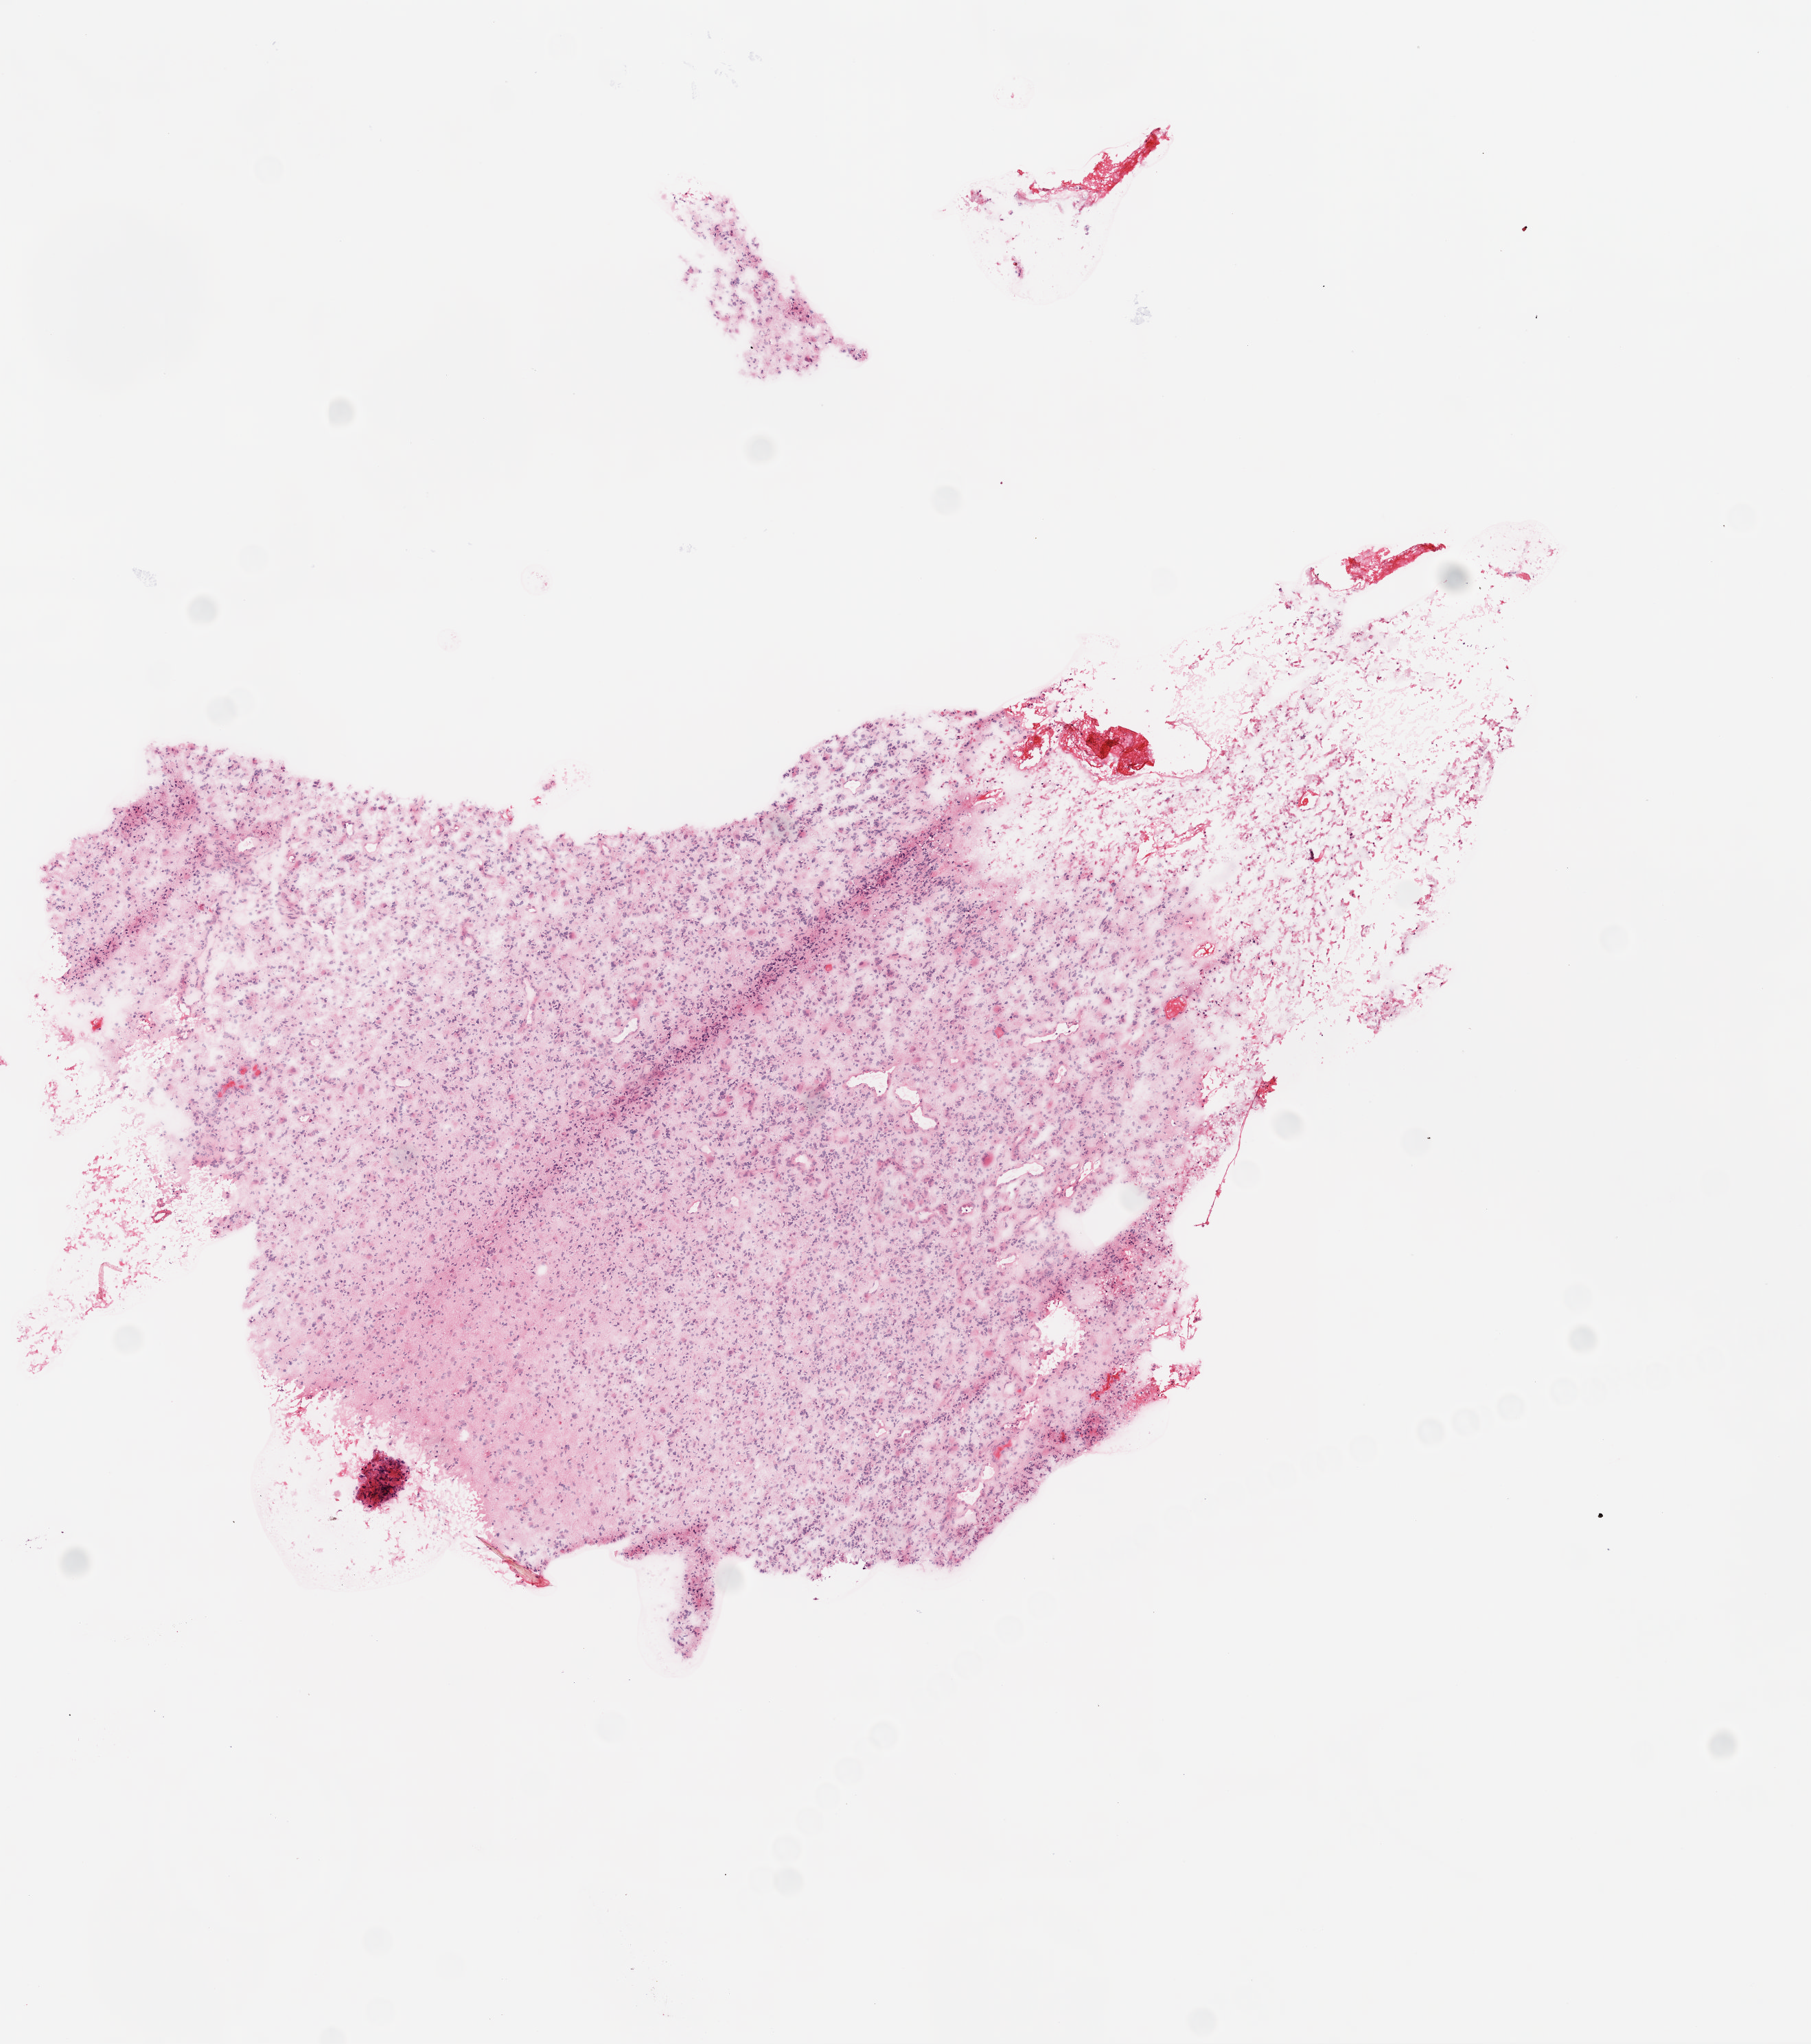
Digitized H&E tissue section (whole slide), whole scanned area (about 5.3 x 6.0 mm, slide scanned at 20x) shown as a low-resolution overview, frozen section from the top of the tissue portion, sample: primary tumour, brain. Male patient; age at initial diagnosis 63 years. Composition of this section per pathologist review: tumour cells 95%, tumour nuclei 90%, normal cells 0%, stromal cells 5%, necrosis 0%.
• pathologic diagnosis: Glioblastoma